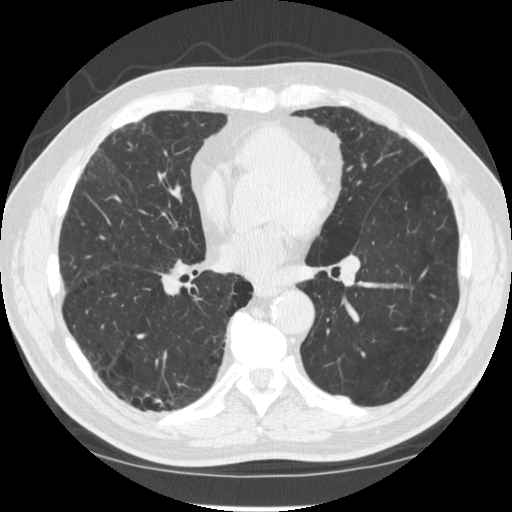
Axial slice from a low-dose chest CT screening exam. Second screening round (one year after baseline). Lung window (W 1500 / L -600 HU). 1.25 mm slice thickness. Standard (soft-tissue) reconstruction kernel (STANDARD). Male, age 70 years at enrolment.
Expert reader's lesion annotation, box from (x=129, y=378) to (x=180, y=430) px. The screening reader recorded 2 non-calcified nodules or masses ≥4 mm on this exam (right lower lobe, right lower lobe); which of them this box marks is not recorded.